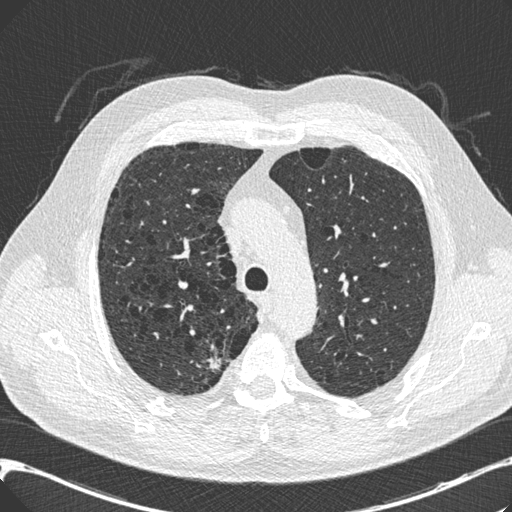
Low-dose screening chest CT, one axial slice; slice 146 of 197 in the series (ordered by position); lung window (W 1500 / L -600 HU); 0.75 mm slice thickness; 512 × 512 image matrix, field of view 367 × 367 mm.
Outlined on this slice (outlined manually by an expert reader):
- lesion 1 (tumor, upper lobe of right lung): bounding box <207,355,221,369> (left, top, right, bottom; pixels)